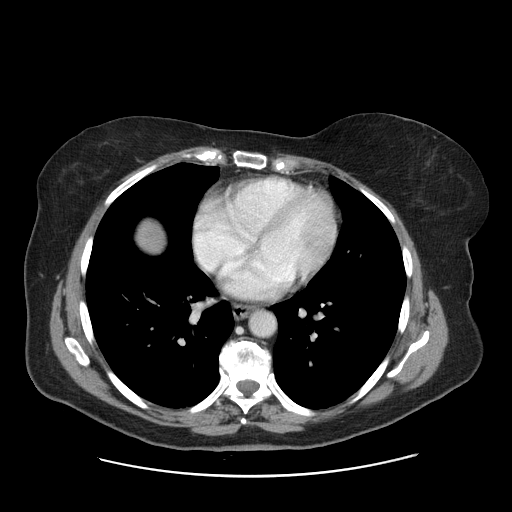
Contrast-enhanced abdominal CT, one axial slice. Position 157 of 161 along the scan axis. 120 kVp. Intravenous contrast given. Soft-tissue window (W 400 / L 40 HU). 2.5 mm slice thickness. 512 × 512 image matrix. Female patient, age 62 years. From the clinical record (not read from this slice): diagnosis: colorectal cancer liver metastases, imaged before liver resection; multiple liver metastases: no; largest metastasis: 2.5 cm.
Outlined on this slice (outlined manually by an expert reader):
- liver: box from (x=136, y=220) to (x=162, y=251) px
- planned liver remnant (the part of the liver to remain after resection): (x=137, y=220)–(x=163, y=252)